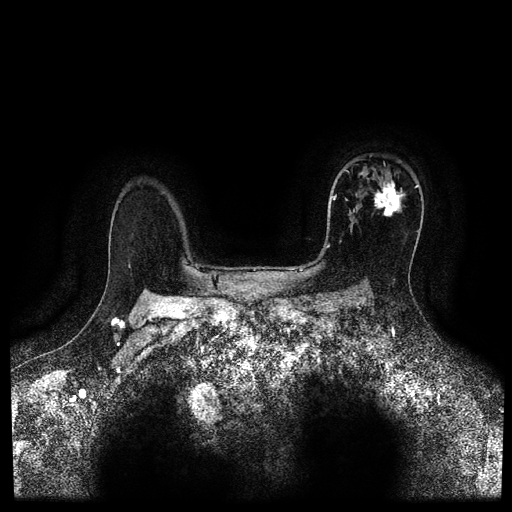
Breast MRI (dynamic contrast-enhanced, multi-phase), one axial slice. Position 75 of 116 along the scan axis. Dynamic contrast-enhanced series, time point 2 of 5 at this slice position (early post-contrast). 1.5 T. TE 2.7 ms, TR 5.4 ms. 512 × 512 image matrix, field of view 340 × 340 mm. Patient: female, 50 years.
Structures marked on this image (semi-automatically segmented with operator editing):
- breast lesion (labelled 'tumour' in the annotation; benign lesions carry a separate 'benign' label): box from (x=373, y=180) to (x=408, y=218) px